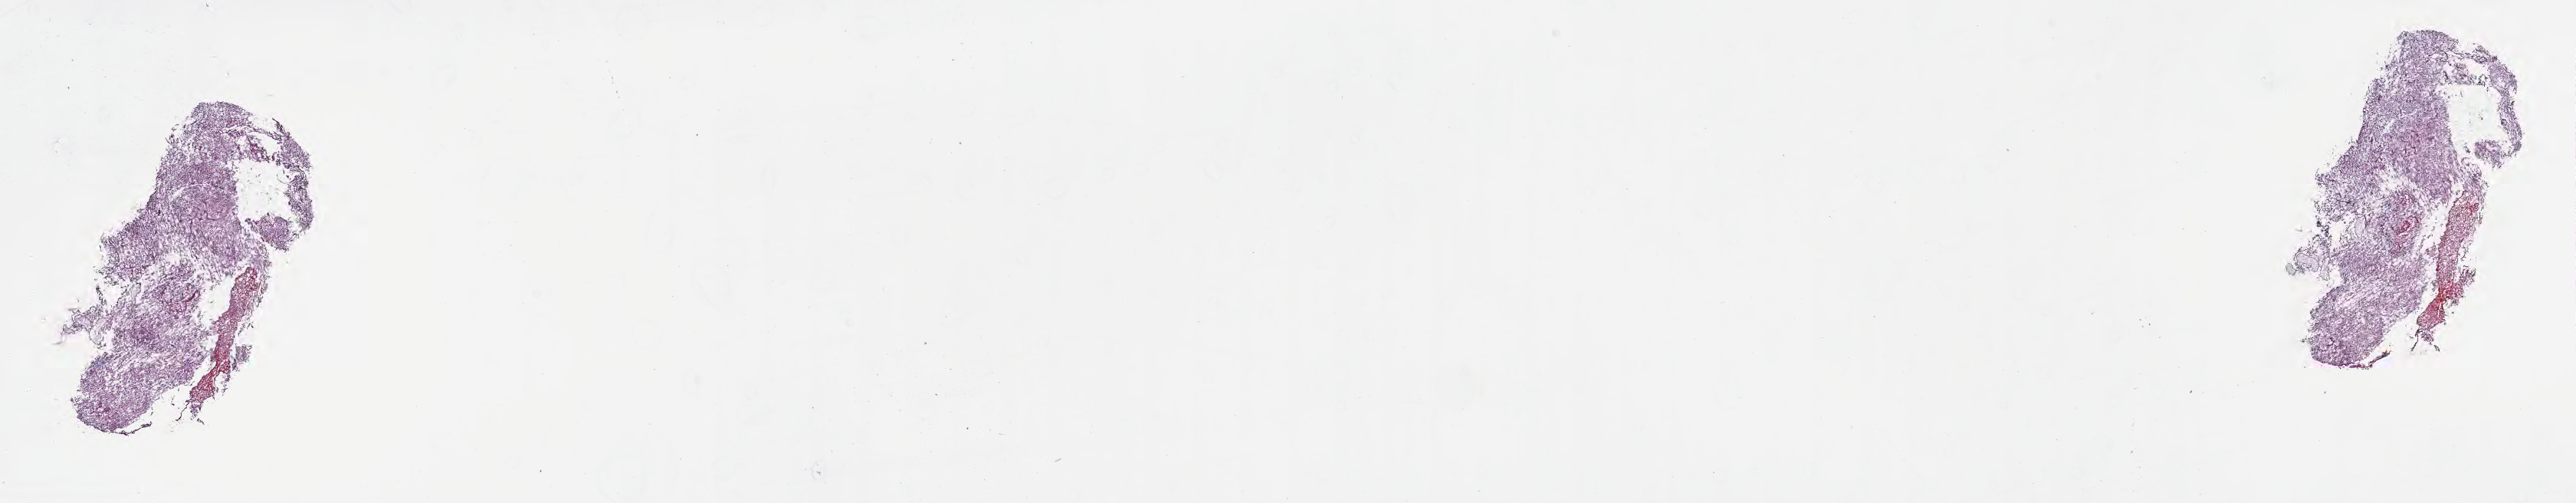
Whole-slide image, hematoxylin and eosin (H&E) stain of tumor tissue from the brain, whole scanned area (about 27.2 x 5.3 mm) shown as a low-resolution overview, frozen section (OCT-embedded). Male patient, age 38 months (3 years 2 months).
Diagnosis (ICD-O-3 morphology term): Craniopharyngioma, NOS.